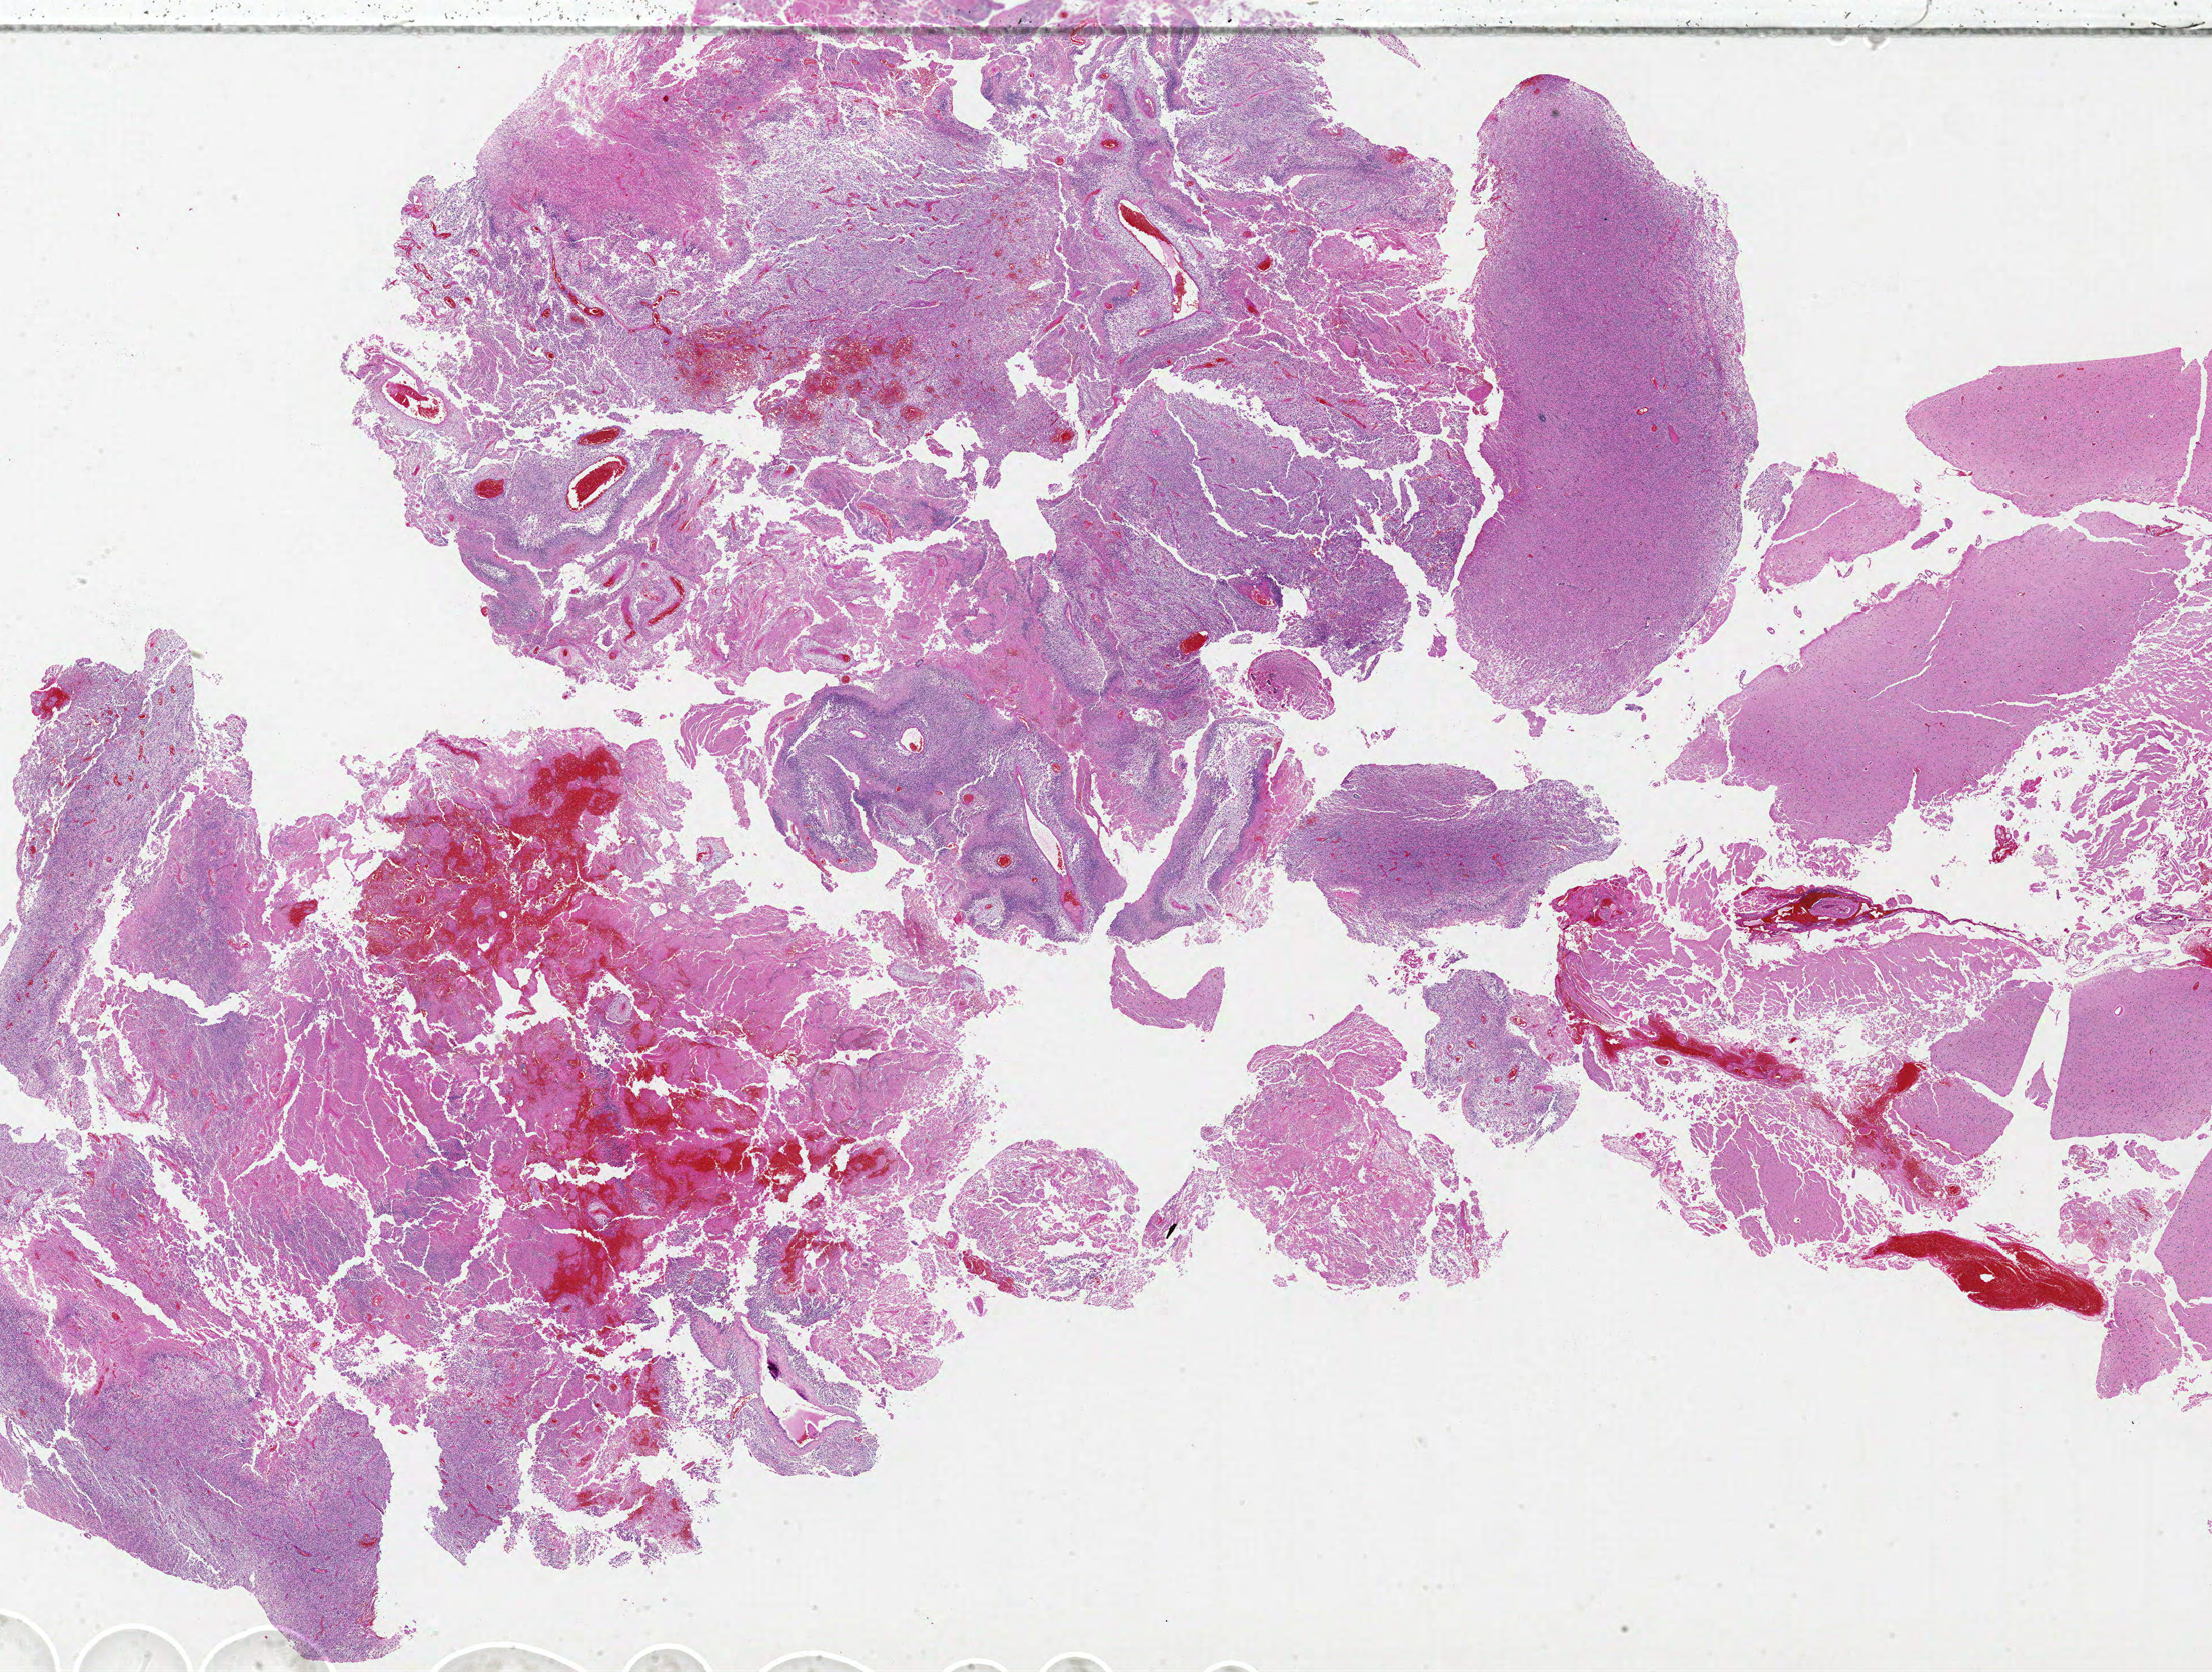
Whole-slide histology image, H&E-stained — a low-resolution overview of the entire scanned area, about 31.0 x 23.4 mm, formalin-fixed paraffin-embedded (FFPE) diagnostic section, sample: primary tumour, brain. Female patient; age at initial diagnosis 47 years.
- diagnosis: Glioblastoma